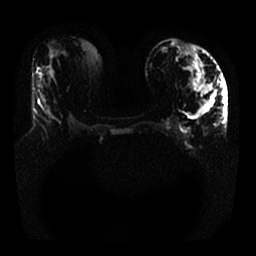
Breast MRI, one axial slice; position 9 of 25 along the scan axis; diffusion-weighted series; image 2 of 4 stored at this slice position (different b-values; order by instance number); 1.5 T; 256 × 256 image matrix. Female patient.
Annotated regions visible in this slice (outlined manually by an expert reader):
- tumour on diffusion-weighted imaging: box from (x=200, y=85) to (x=216, y=114) px